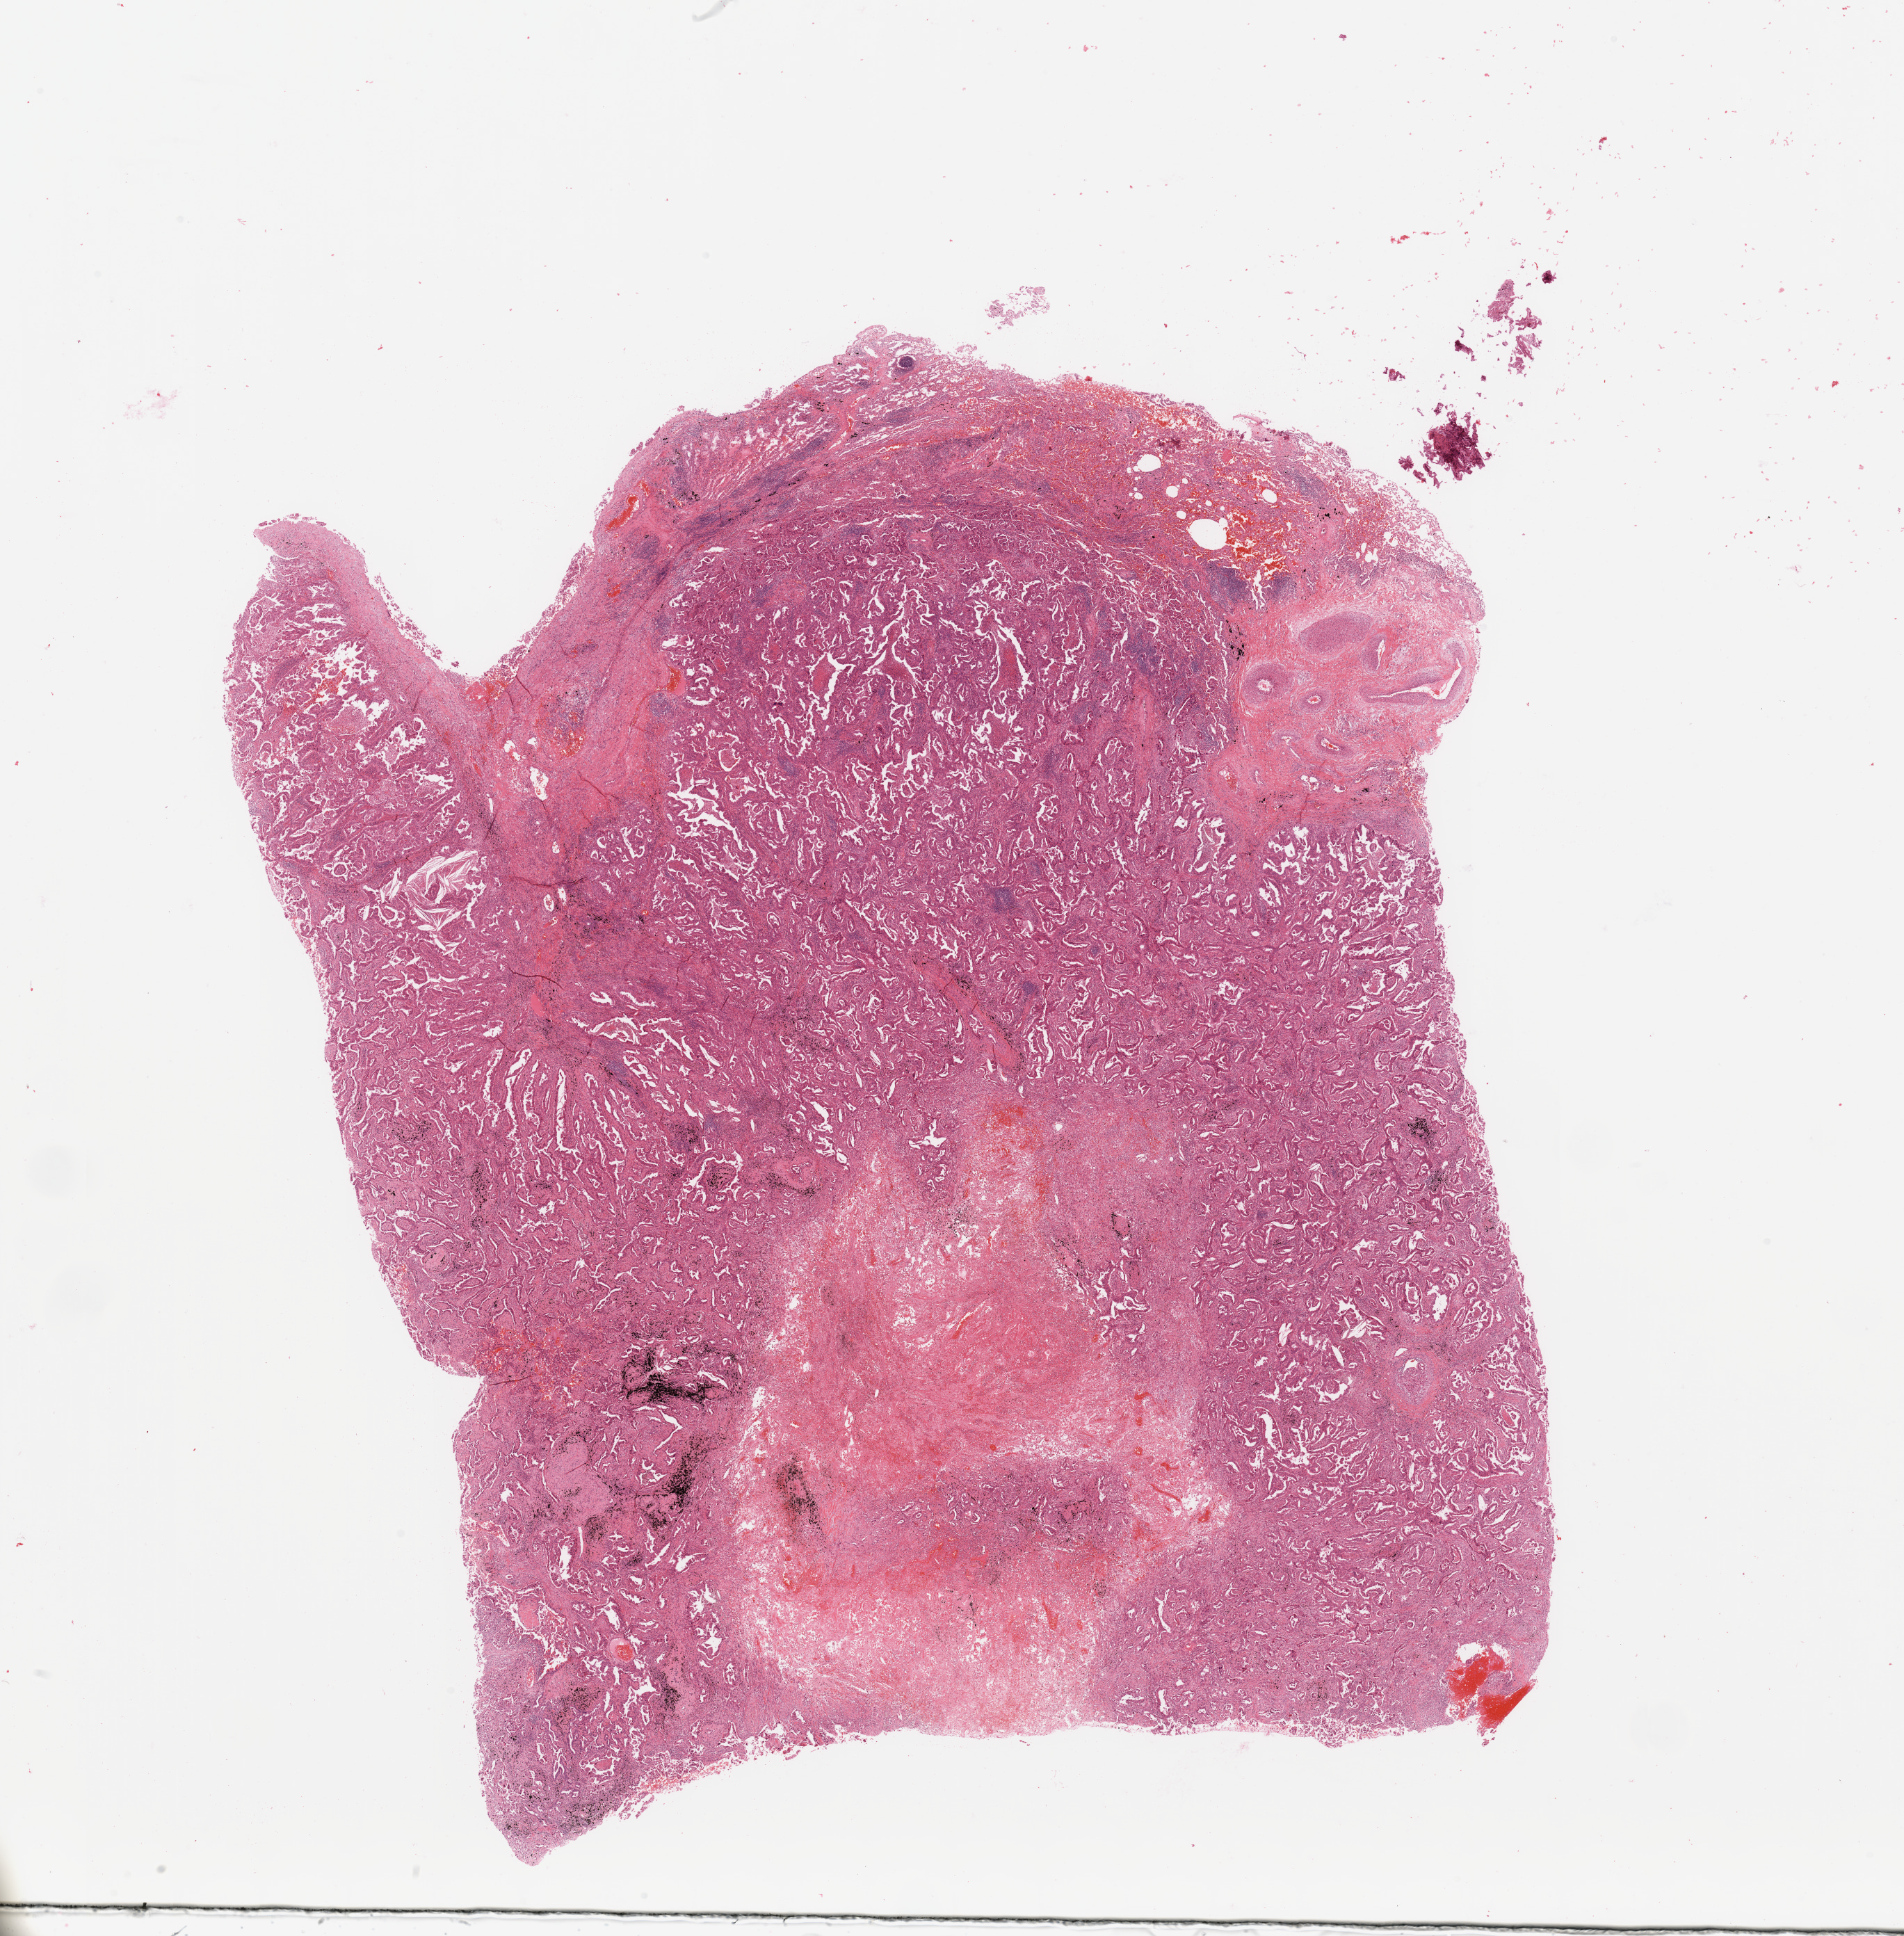
Hematoxylin and eosin (H&E) stained whole-slide image — a low-resolution overview of the entire scanned area, about 21.7 x 22.0 mm (slide scanned at 20x). Lung, tumour tissue. Patient: male, age 72 years.
Diagnosis: Adenocarcinoma, NOS.